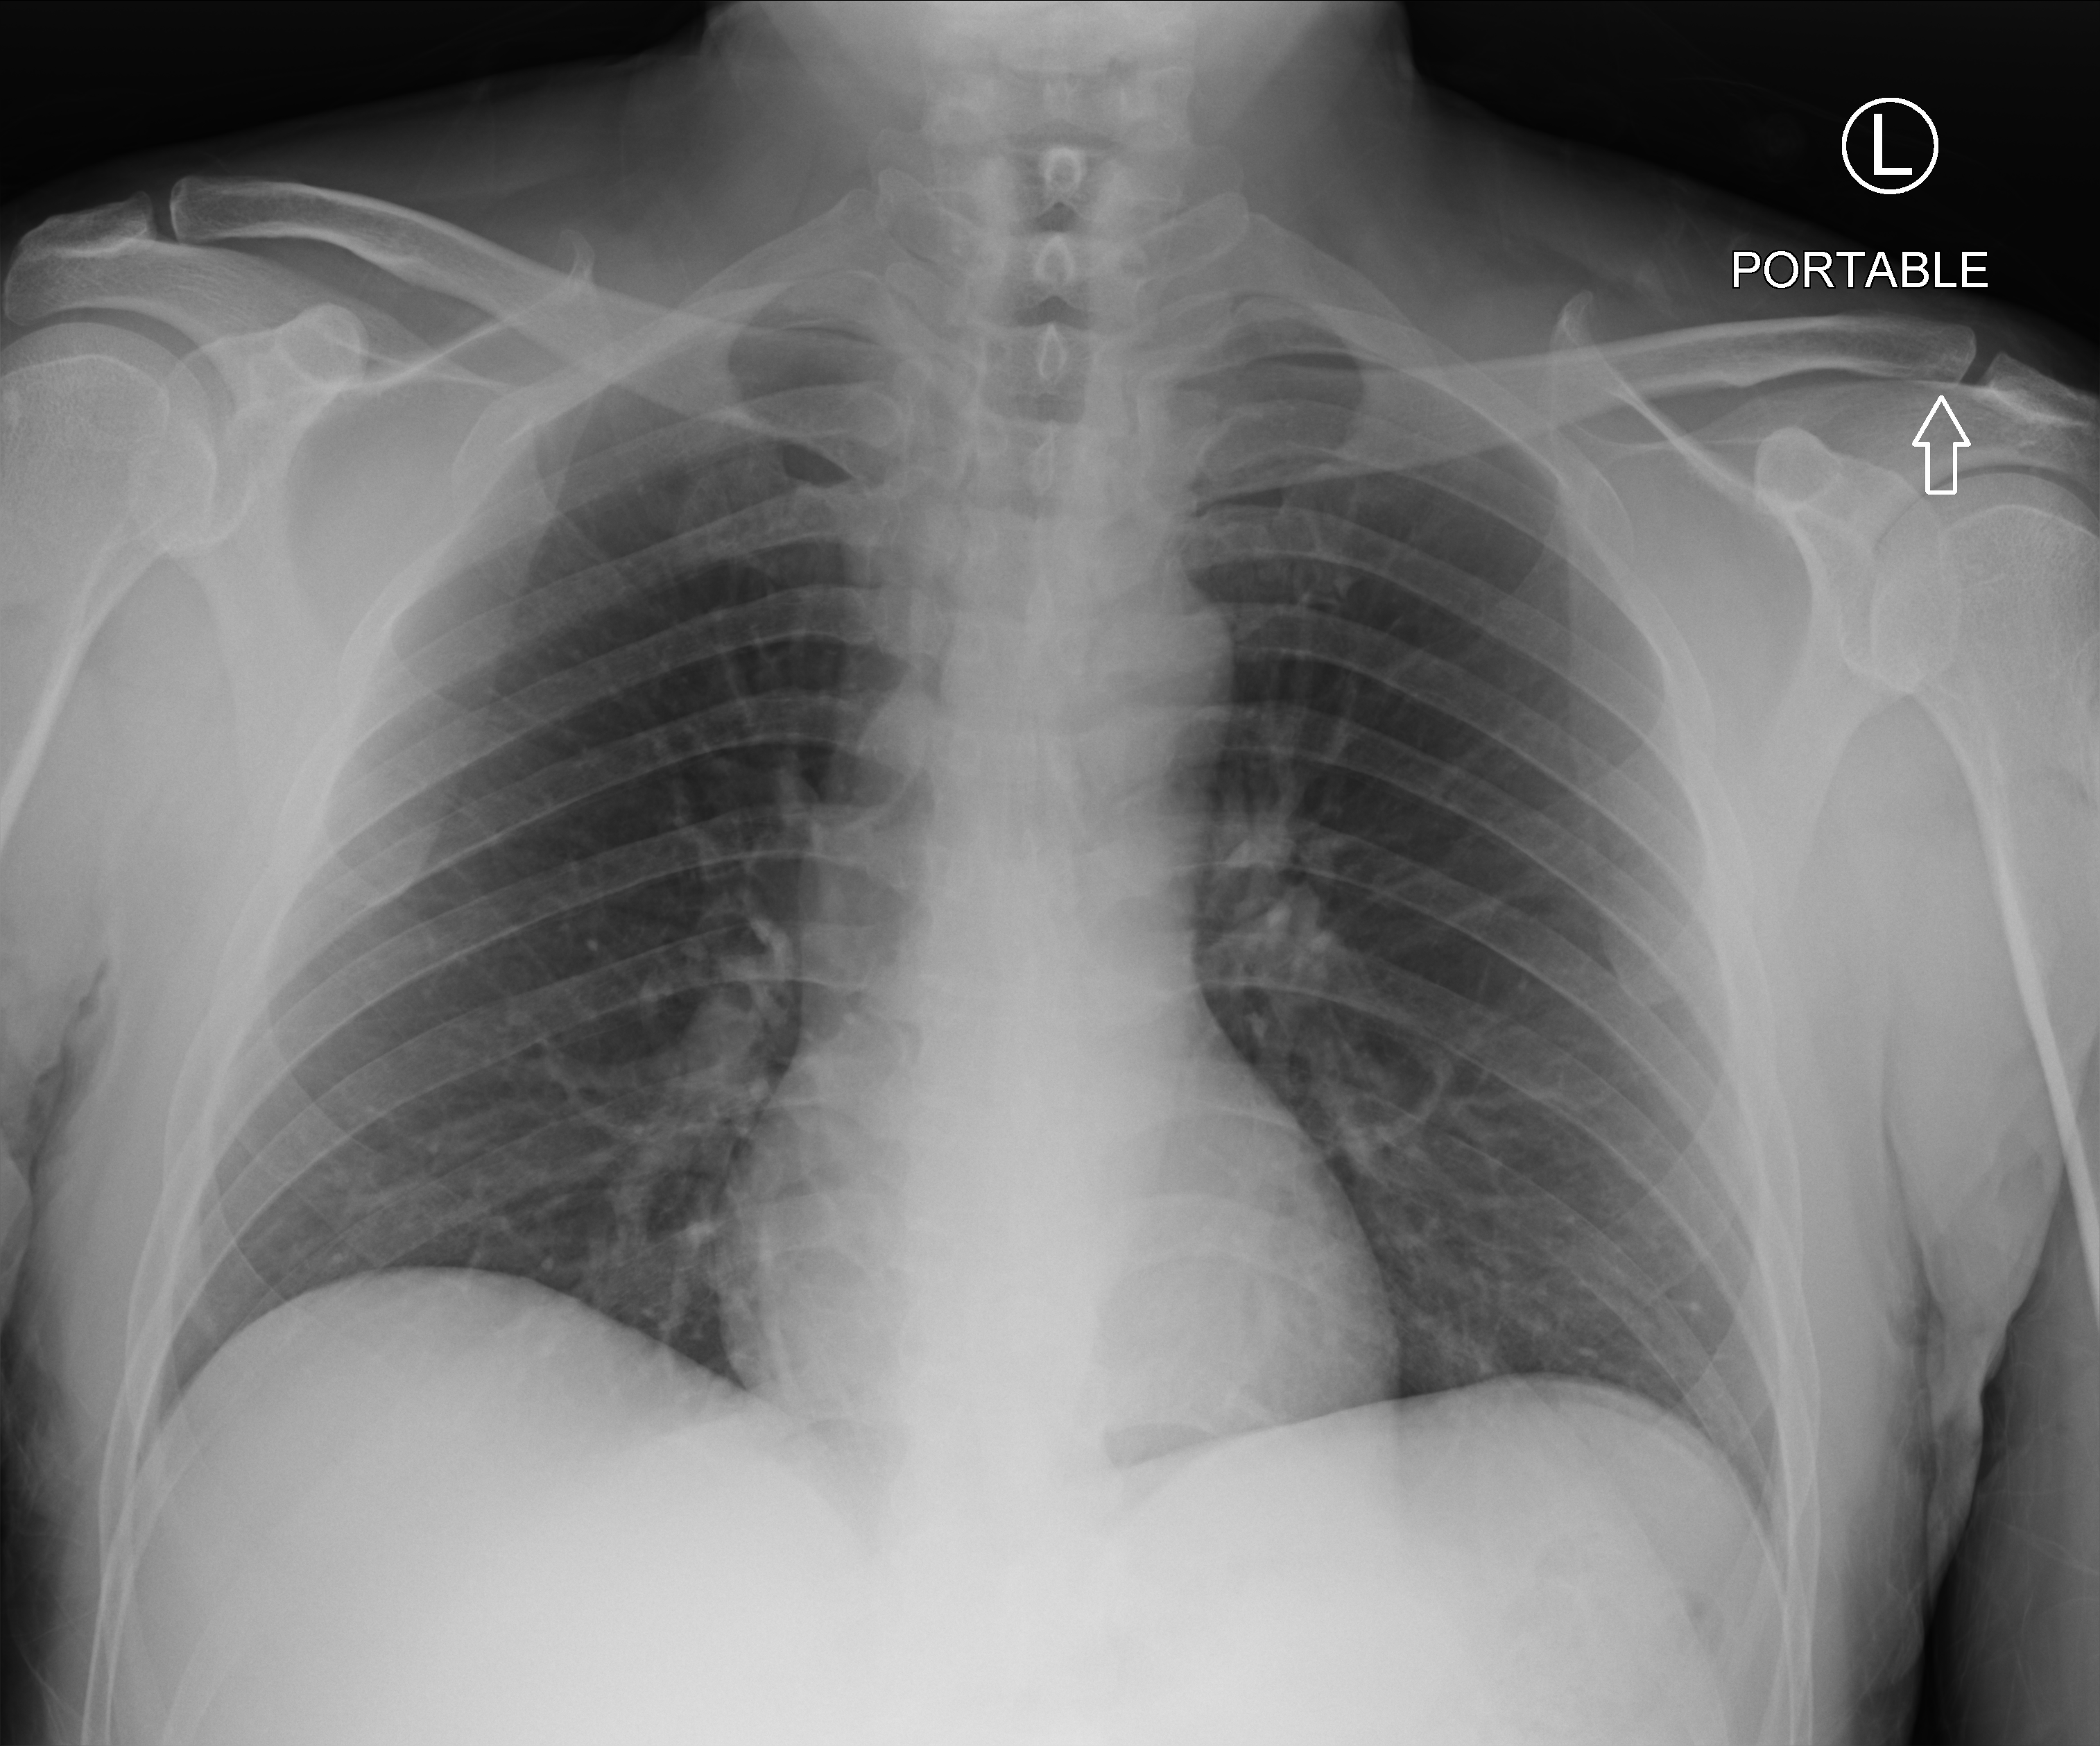
Chest X-ray (portable), anteroposterior (AP) projection. Male patient hospitalised with COVID-19, age 18–59 years.
Admission-level facts for this patient (not findings on this image; timing relative to this image not recorded):
- mechanically ventilated during this hospital stay: no
- admitted to intensive care during this hospital stay: no